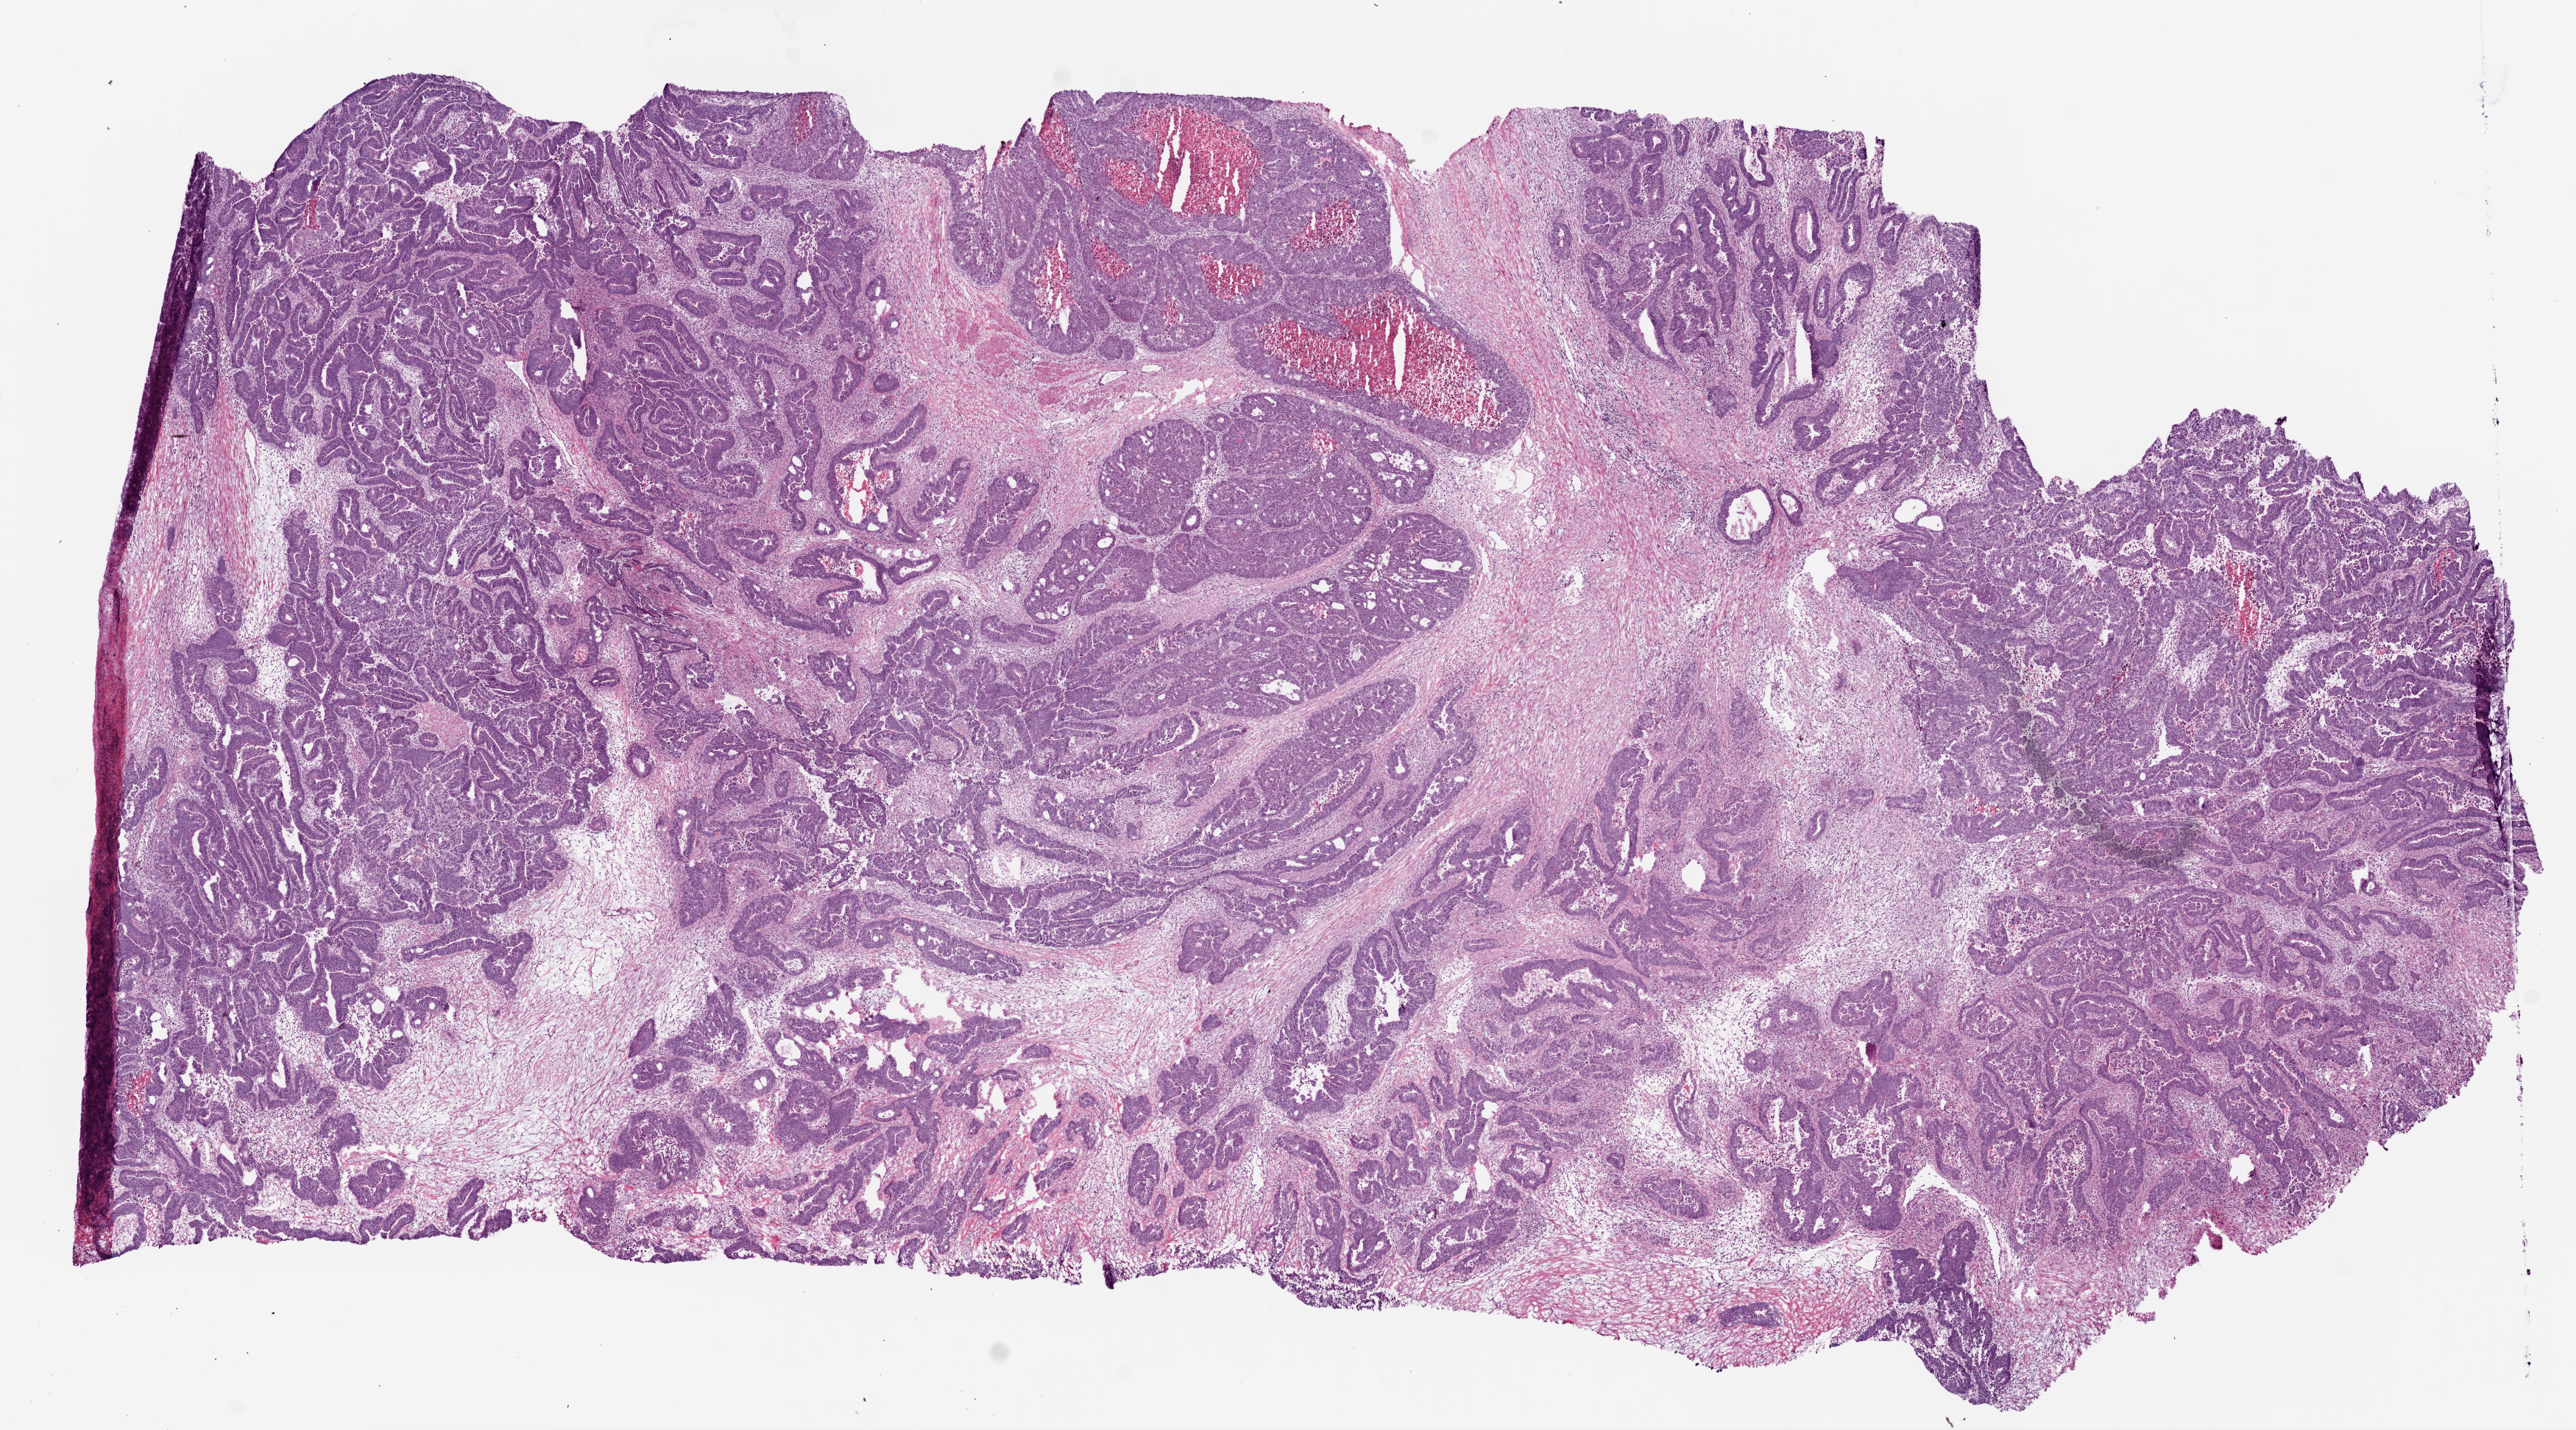
Digitized Hematoxylin and eosin (H&E) stained tissue section (whole slide) — low-resolution overview of the scanned area, about 14.0 x 7.8 mm, frozen section from the bottom of the tissue portion, sample: primary tumour, colon. Male patient; age at initial diagnosis 73 years. Composition of this section per pathologist review: tumour cells 92%, tumour nuclei 90%, normal cells 0%, stromal cells 4%, necrosis 4%. Inflammatory infiltration, as recorded: lymphocyte infiltration 5%, monocyte infiltration 0%, neutrophil infiltration 2%.
* pathologic diagnosis: Adenocarcinoma, NOS (ascending colon)
* AJCC pathologic stage: IIIC
* TNM: T3 N2b M0
* lymph nodes positive (case pathology): 11 of 23 examined